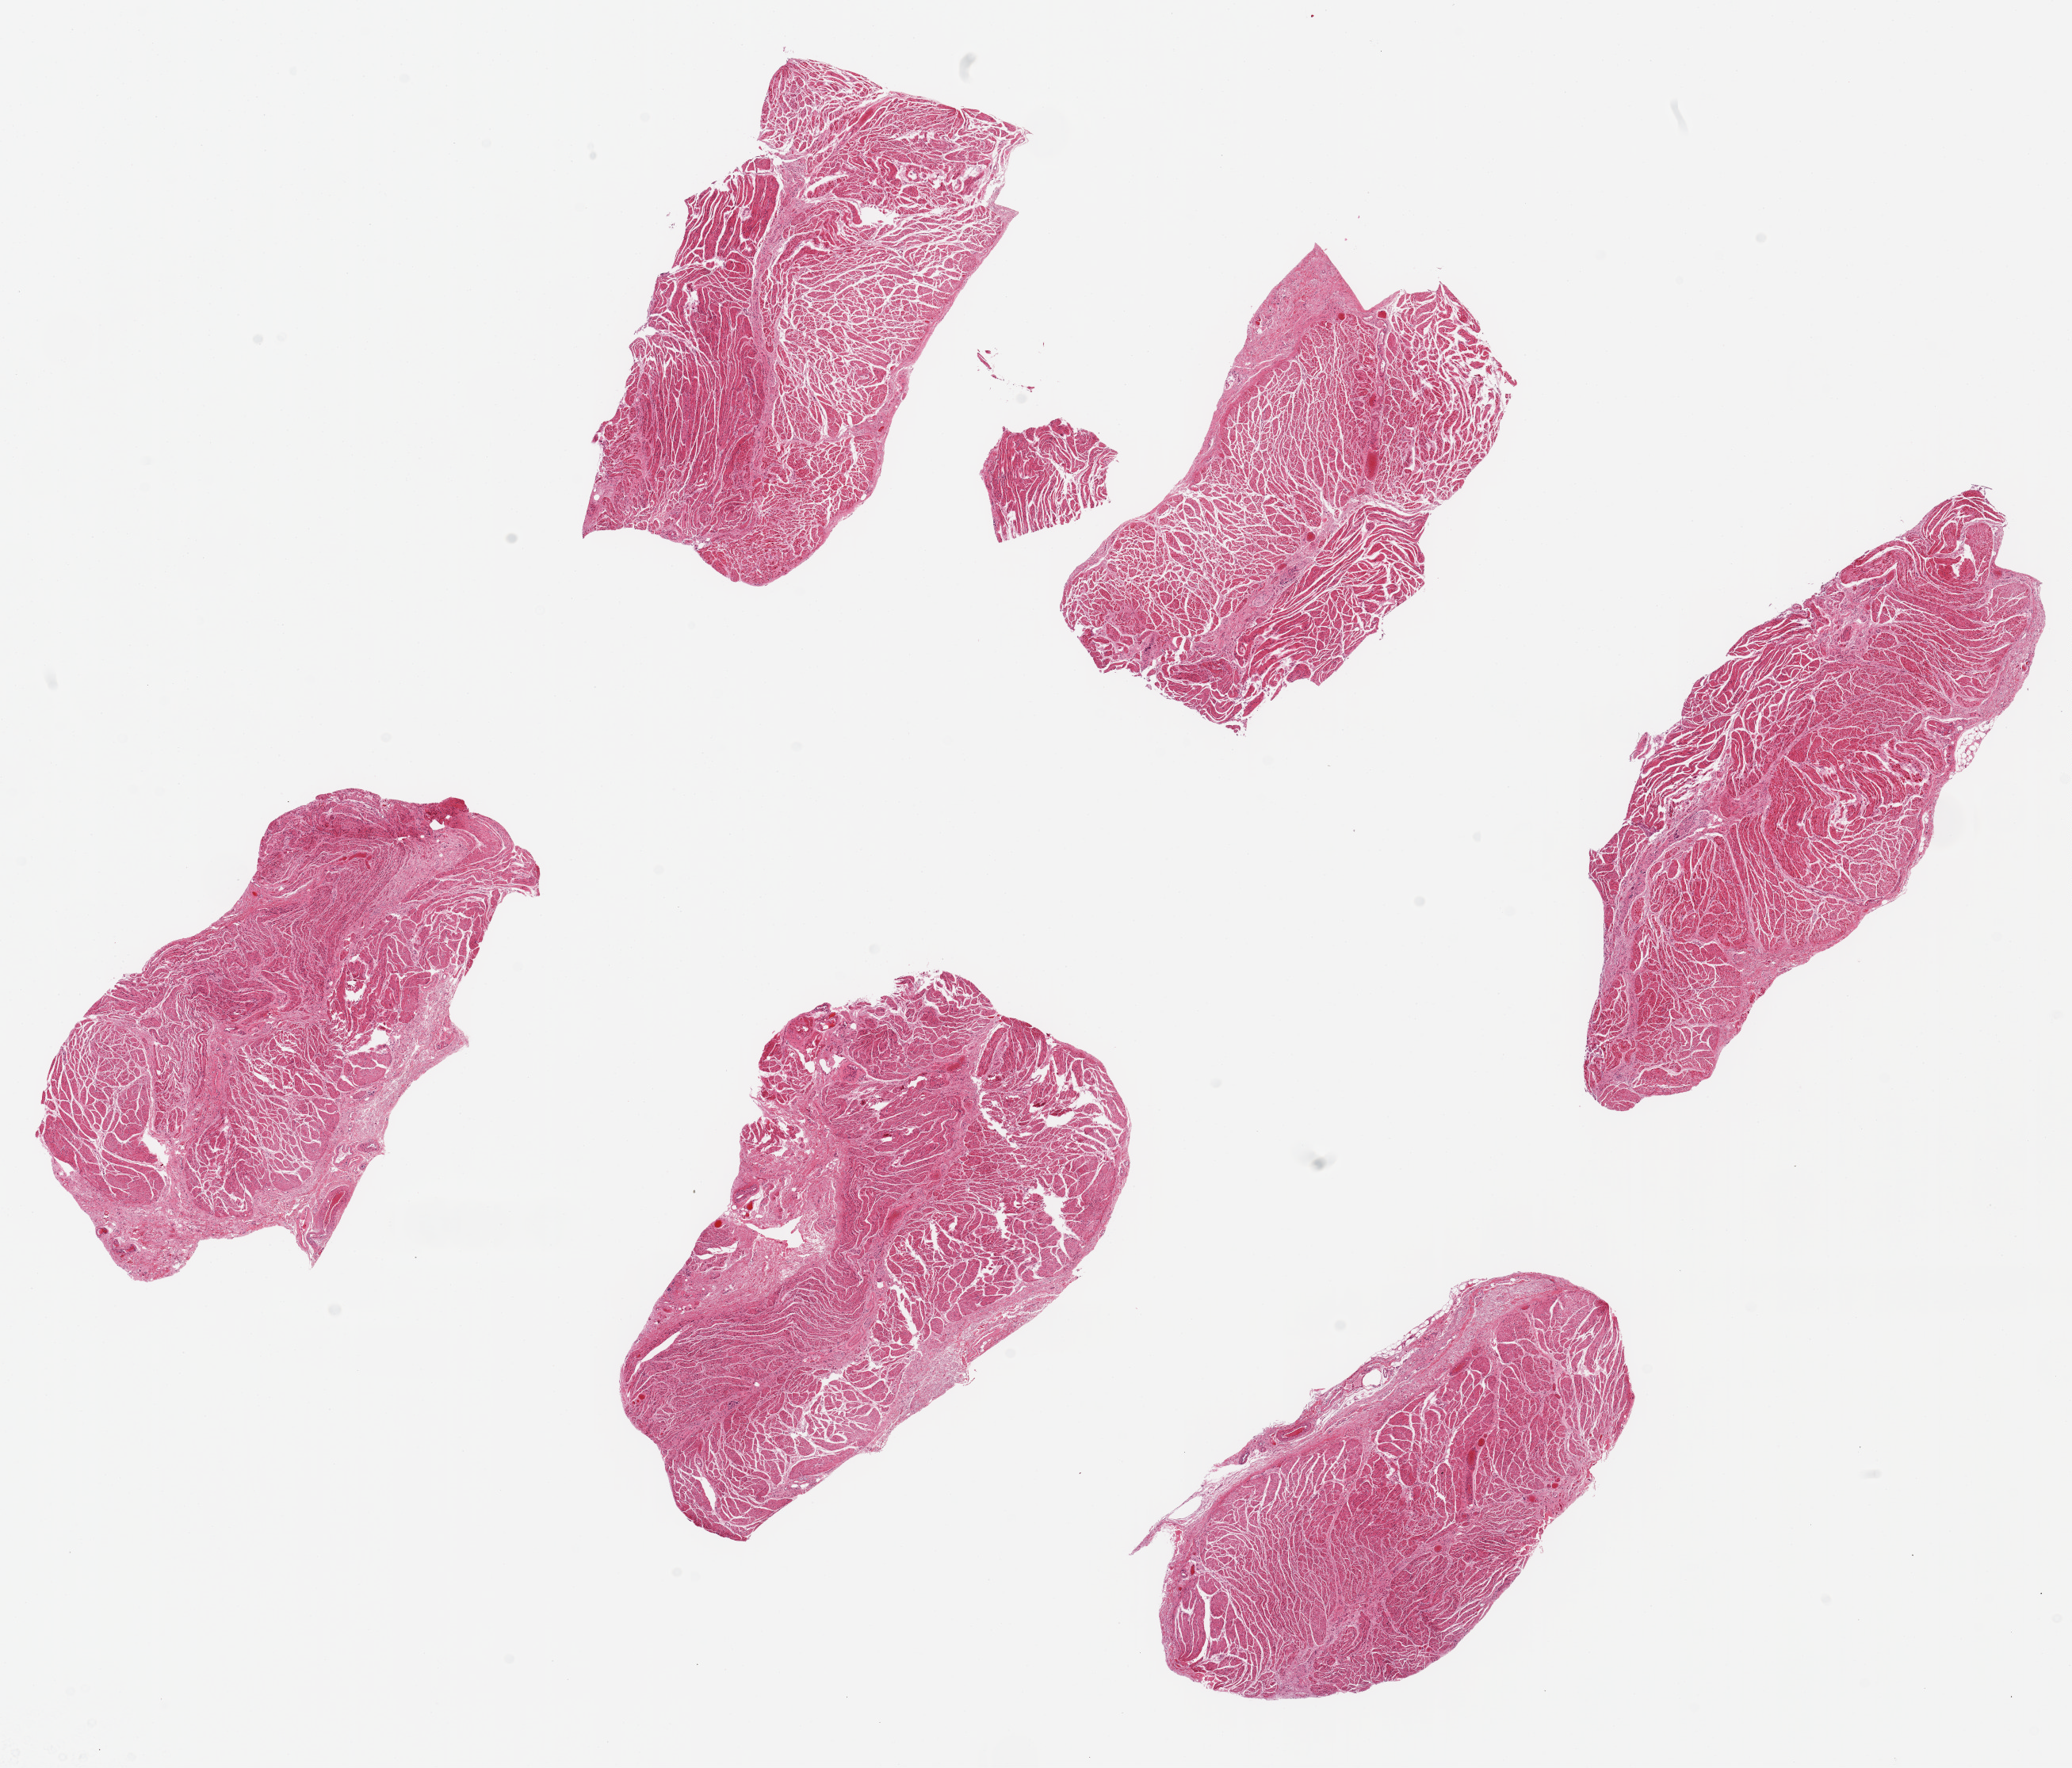
Digitized hematoxylin and eosin (H&E)-stained section, shown as a low-resolution overview of the whole scanned area (about 20.7 x 17.6 mm); PAXgene-fixed paraffin-embedded (PFPE) section; sampled site (target tissue): esophageal muscle; donor tissue sample. Female donor.
- reviewer comment on this tissue sample: 6 ~ 5.5x3mm pieces